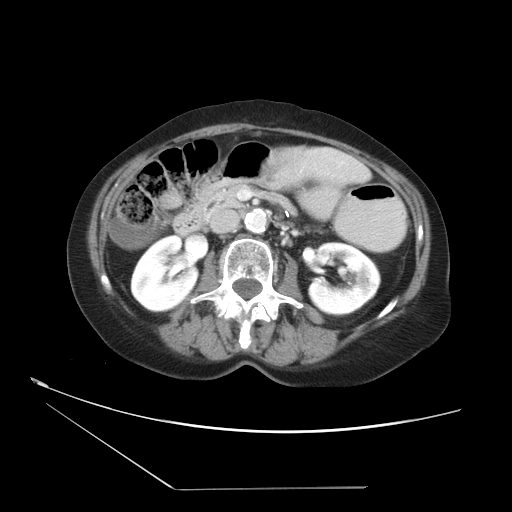
Contrast-enhanced abdominal CT, one axial slice; position 12 of 36 along the scan axis; 120 kVp; intravenous contrast given; soft-tissue window (W 400 / L 40 HU); 5 mm slice thickness; 512 × 512 image matrix, field of view 384 × 384 mm. Female patient, age 81 years. From the clinical record (not read from this slice): diagnosis: colorectal cancer liver metastases, imaged before liver resection; multiple liver metastases: no; largest metastasis: 1.6 cm; disease in both lobes: no.
Outlined on this slice (outlined manually by an expert reader):
- liver: bounding box [x1, y1, x2, y2] px = [163, 148, 371, 206]
- planned liver remnant (the part of the liver to remain after resection): [164, 168, 371, 205]